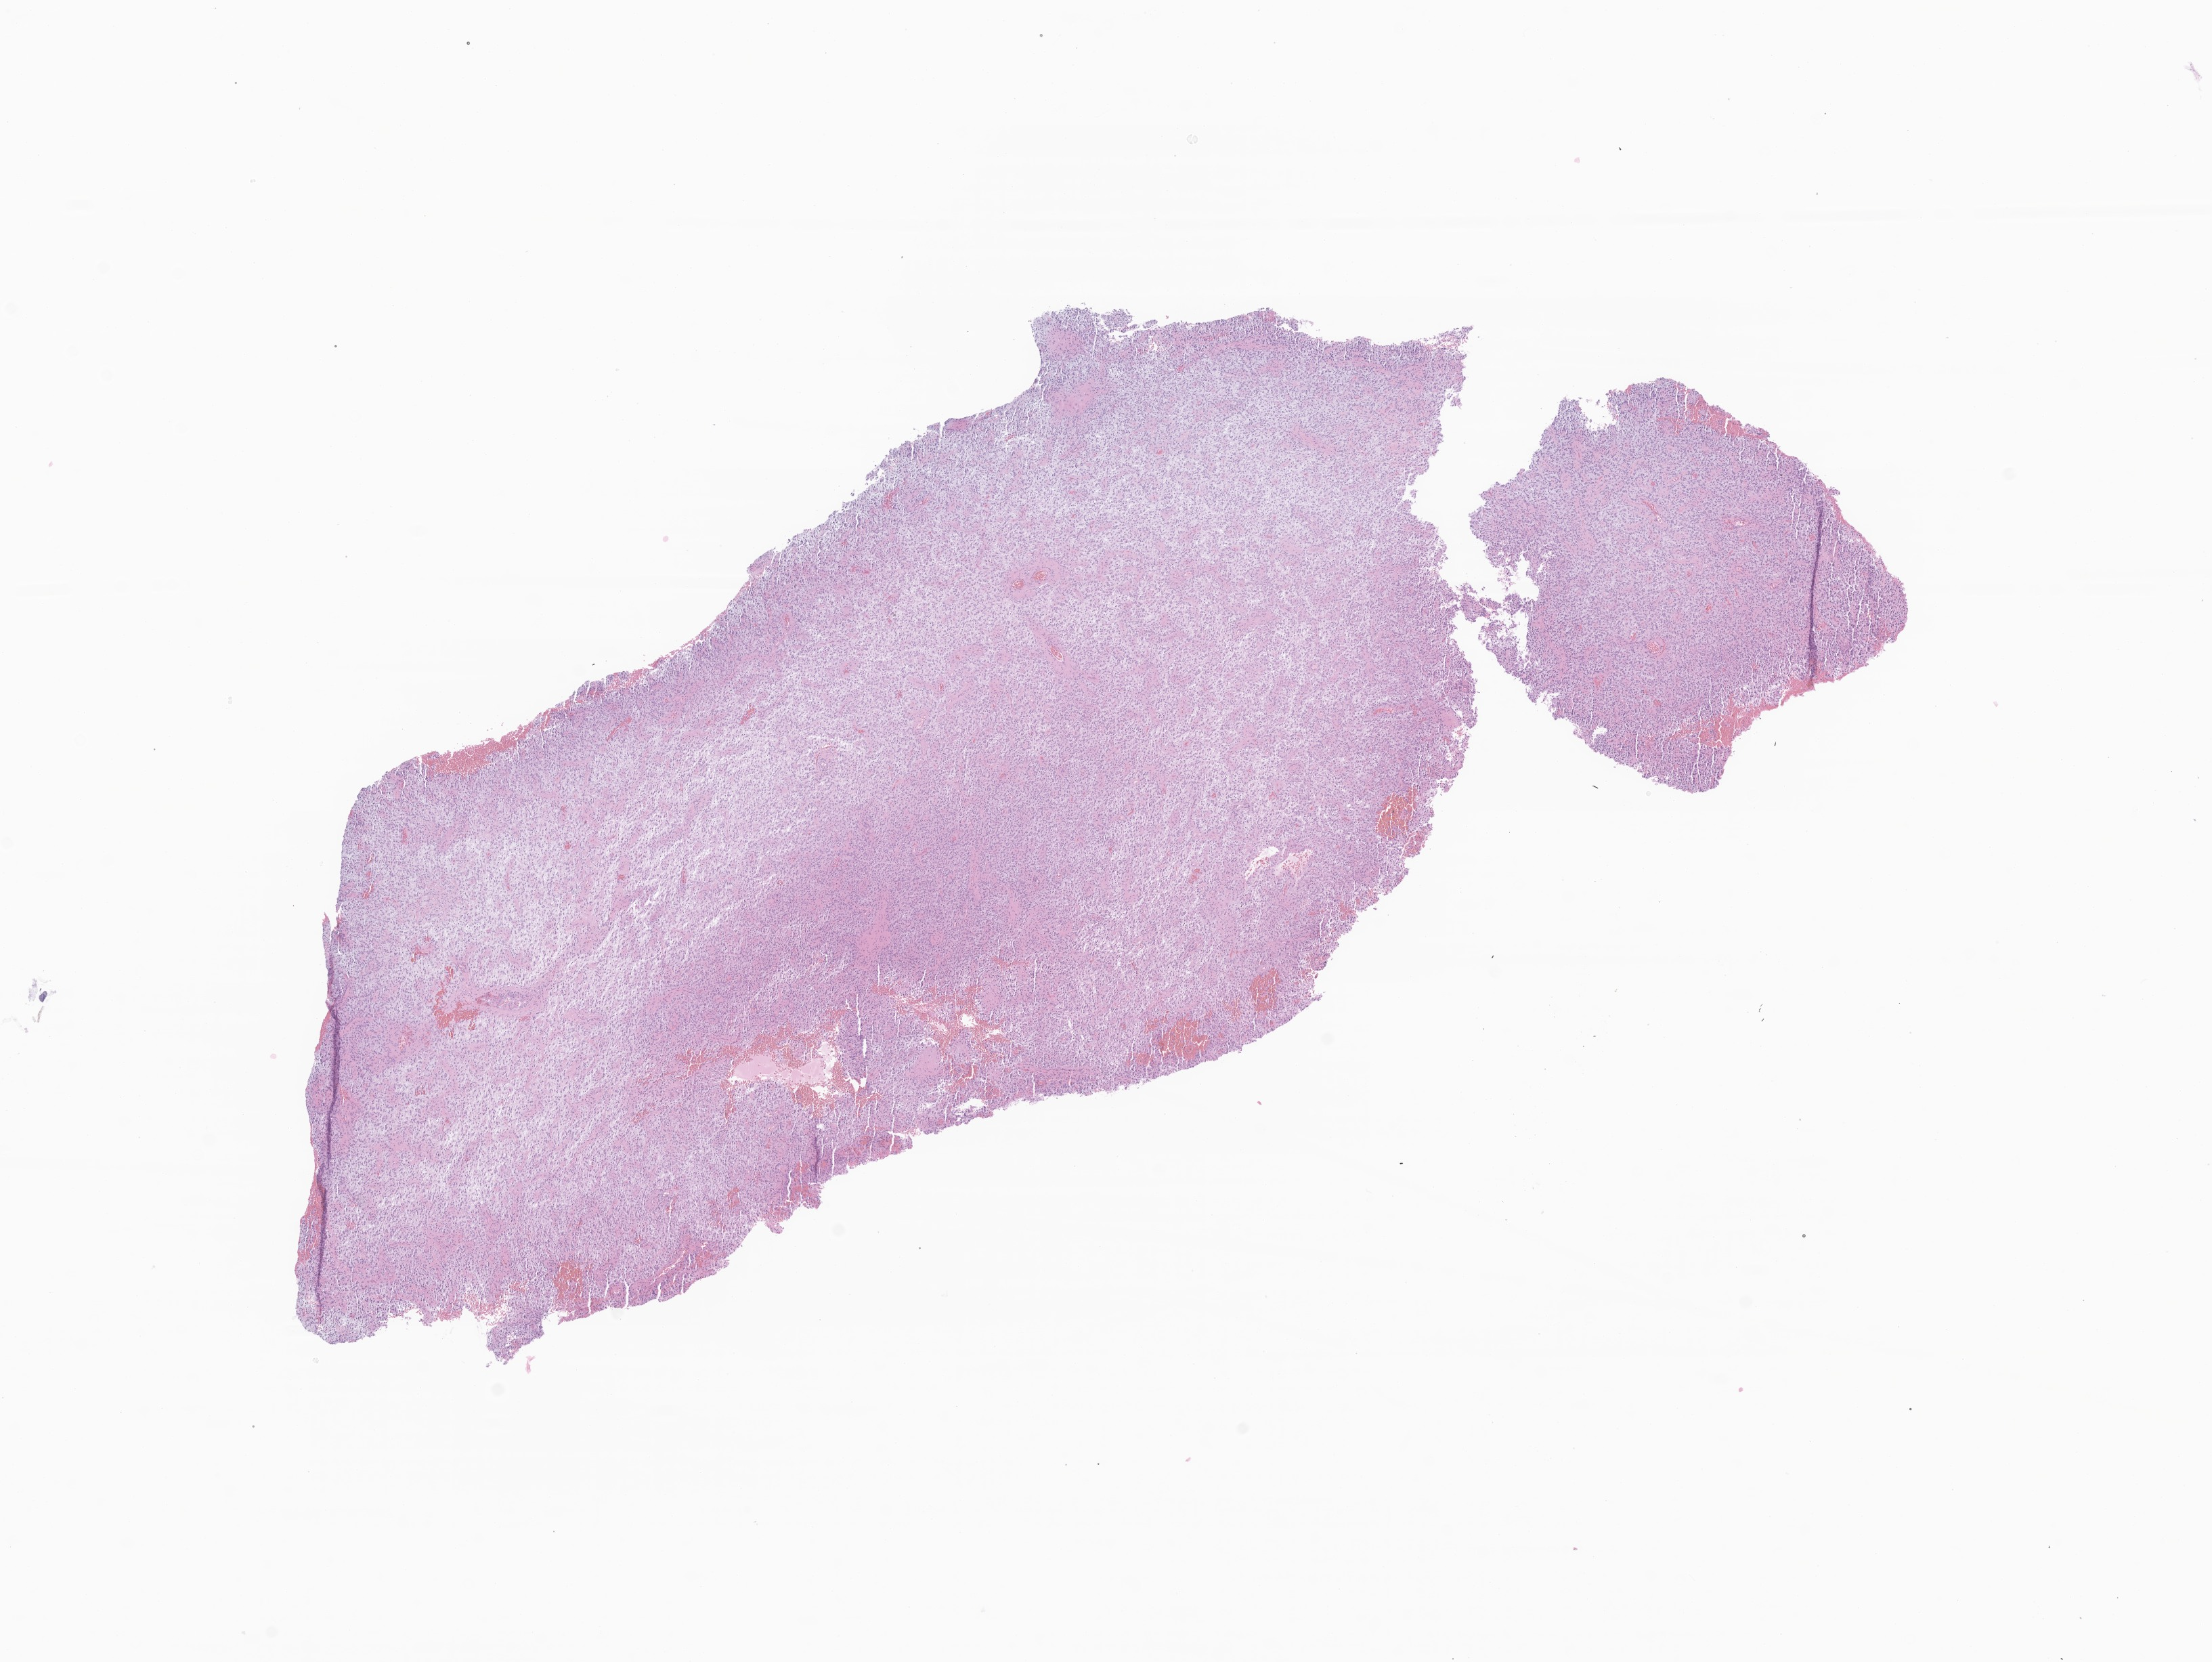
Haematoxylin and eosin whole-slide image of tumor tissue from the cerebellum, whole scanned area (about 13.8 x 10.3 mm) shown as a low-resolution overview; FFPE section. Patient: female, age 92 months.
* diagnosis (ICD-O-3 morphology term): Glioma, malignant